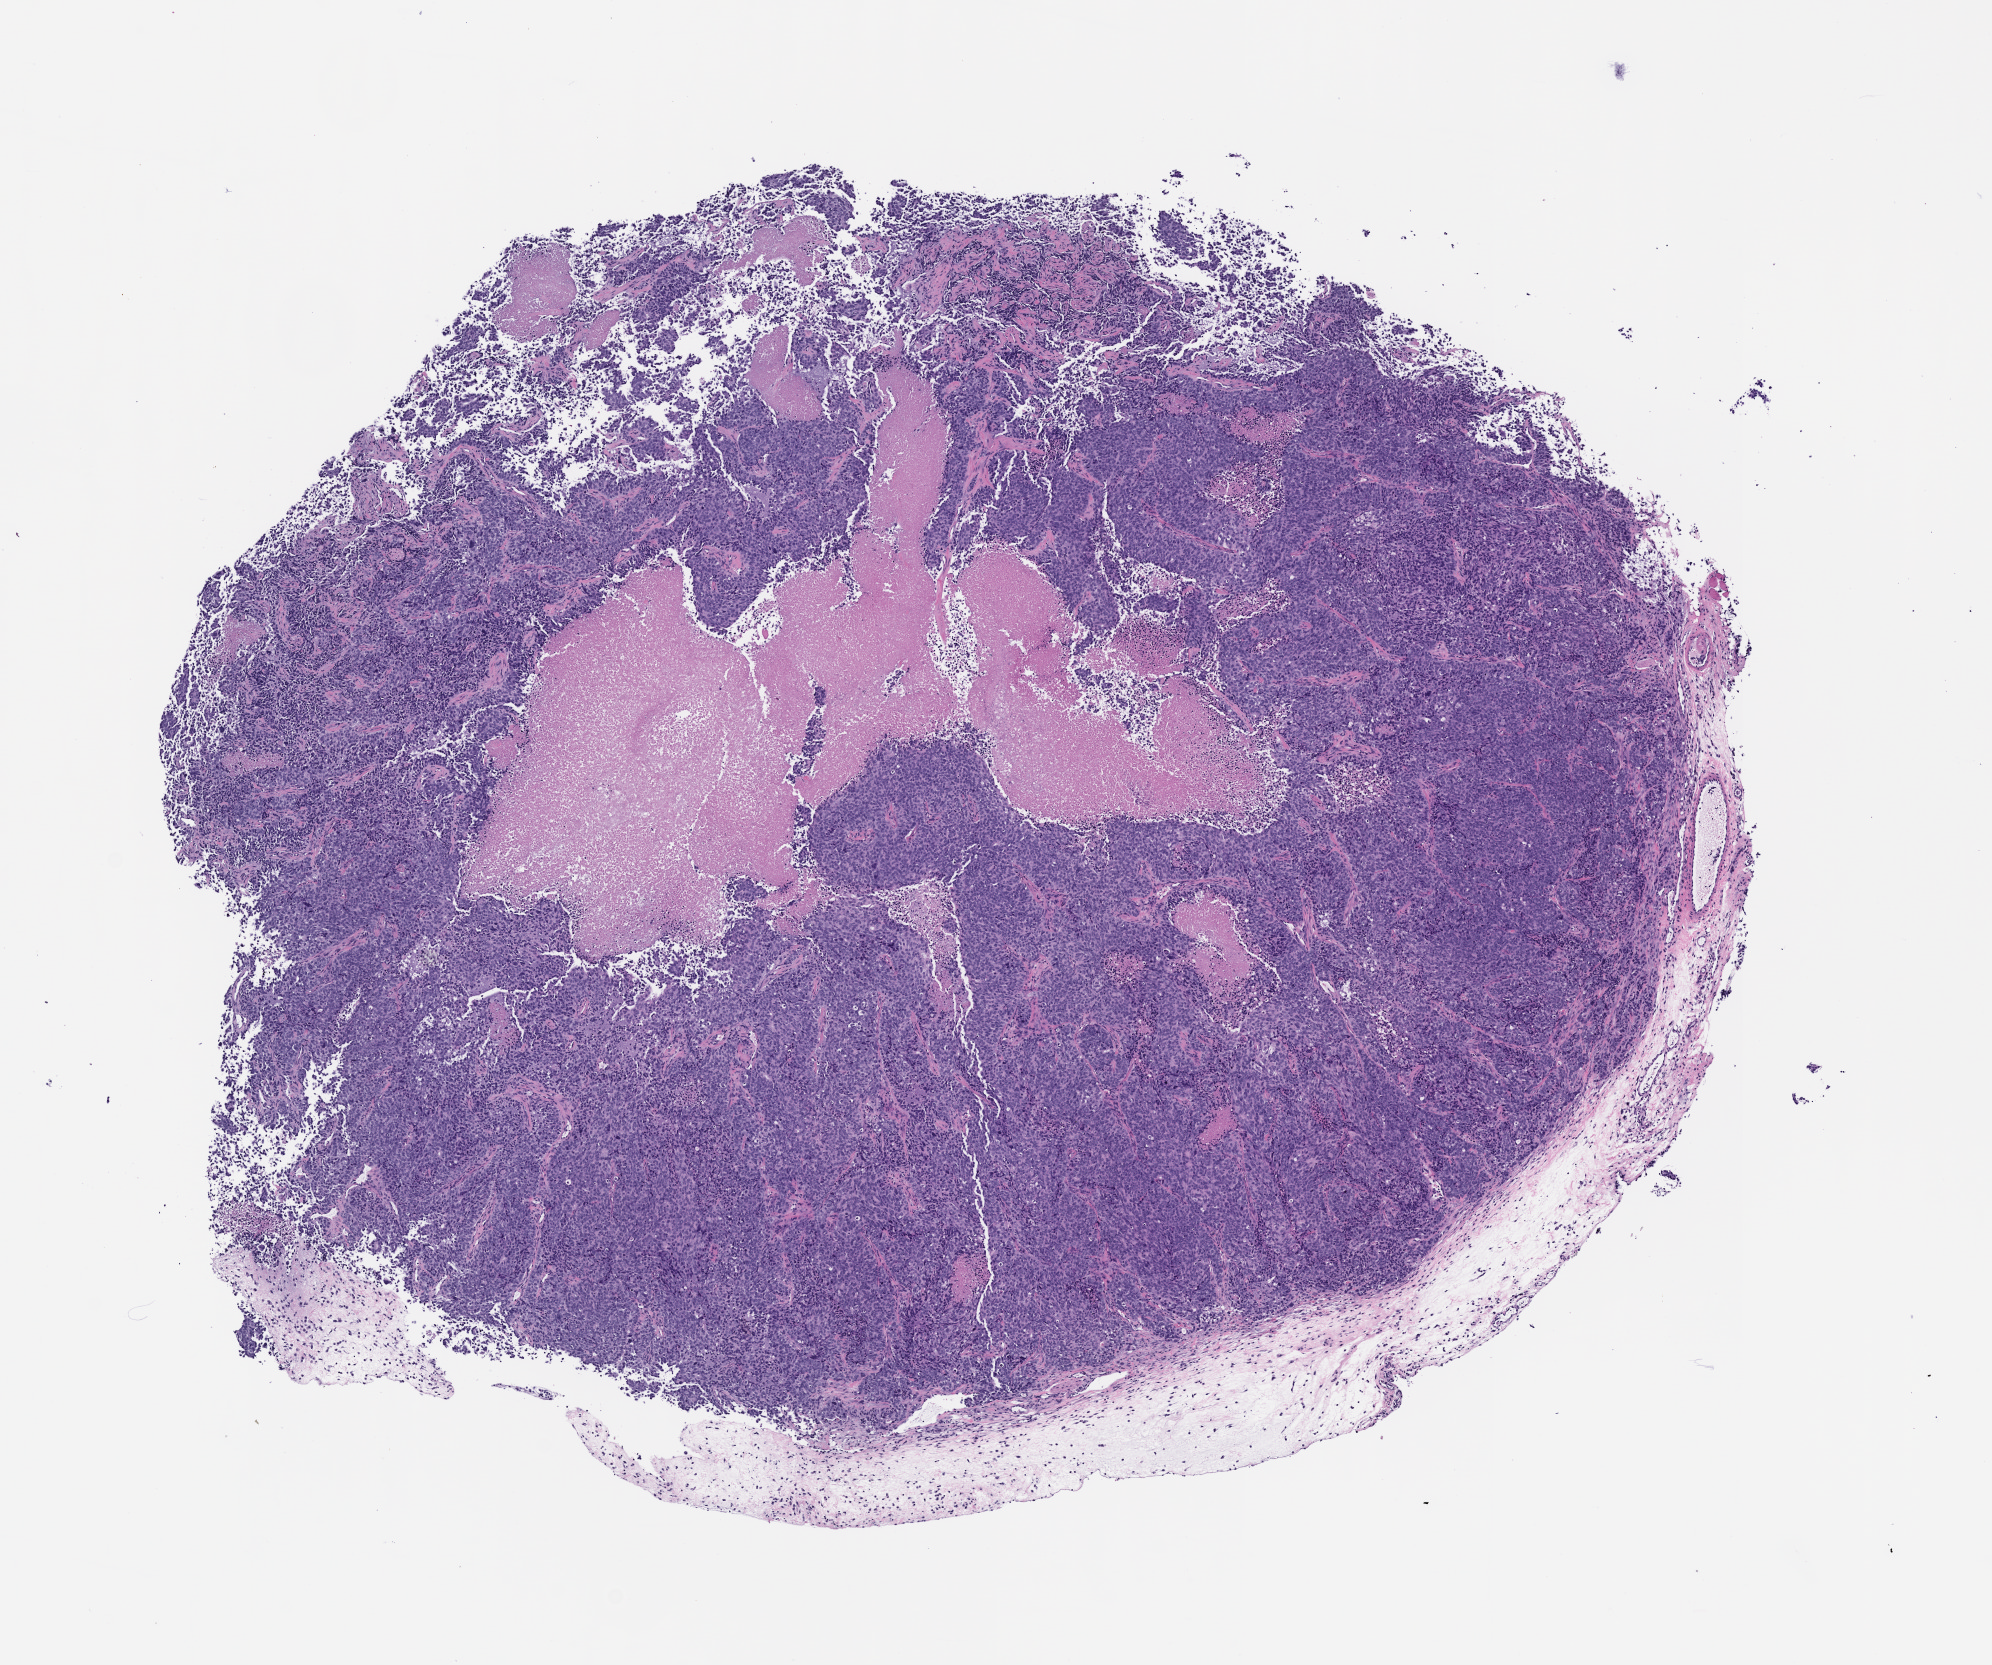
Whole-slide image, haematoxylin and eosin: patient-derived xenograft (human tumor grown in a mouse), passage 2 — low-resolution overview of the scanned area, about 8.0 x 6.7 mm, formalin-fixed paraffin-embedded section, originating tumor site category: cervix.
Originating patient diagnosis: Cervical Adenocarcinoma.